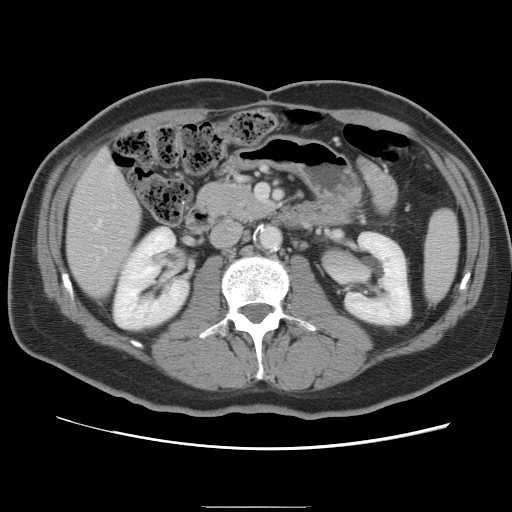
Contrast-enhanced abdominal CT, one axial slice. Position 30 of 87 along the scan axis. 120 kVp. Soft-tissue window (W 400 / L 40 HU). 5 mm slice thickness. 512 × 512 image matrix. Male patient, age 63 years. Case-level facts recorded for this patient, not image findings: diagnosis: colorectal cancer liver metastases, imaged before liver resection; multiple liver metastases: no.
Annotated regions visible in this slice (outlined manually by an expert reader):
- hepatic veins: bounding box <95,221,101,229> (left, top, right, bottom; pixels)
- liver: <68,152,141,297>
- planned liver remnant (the part of the liver to remain after resection): <68,152,141,299>